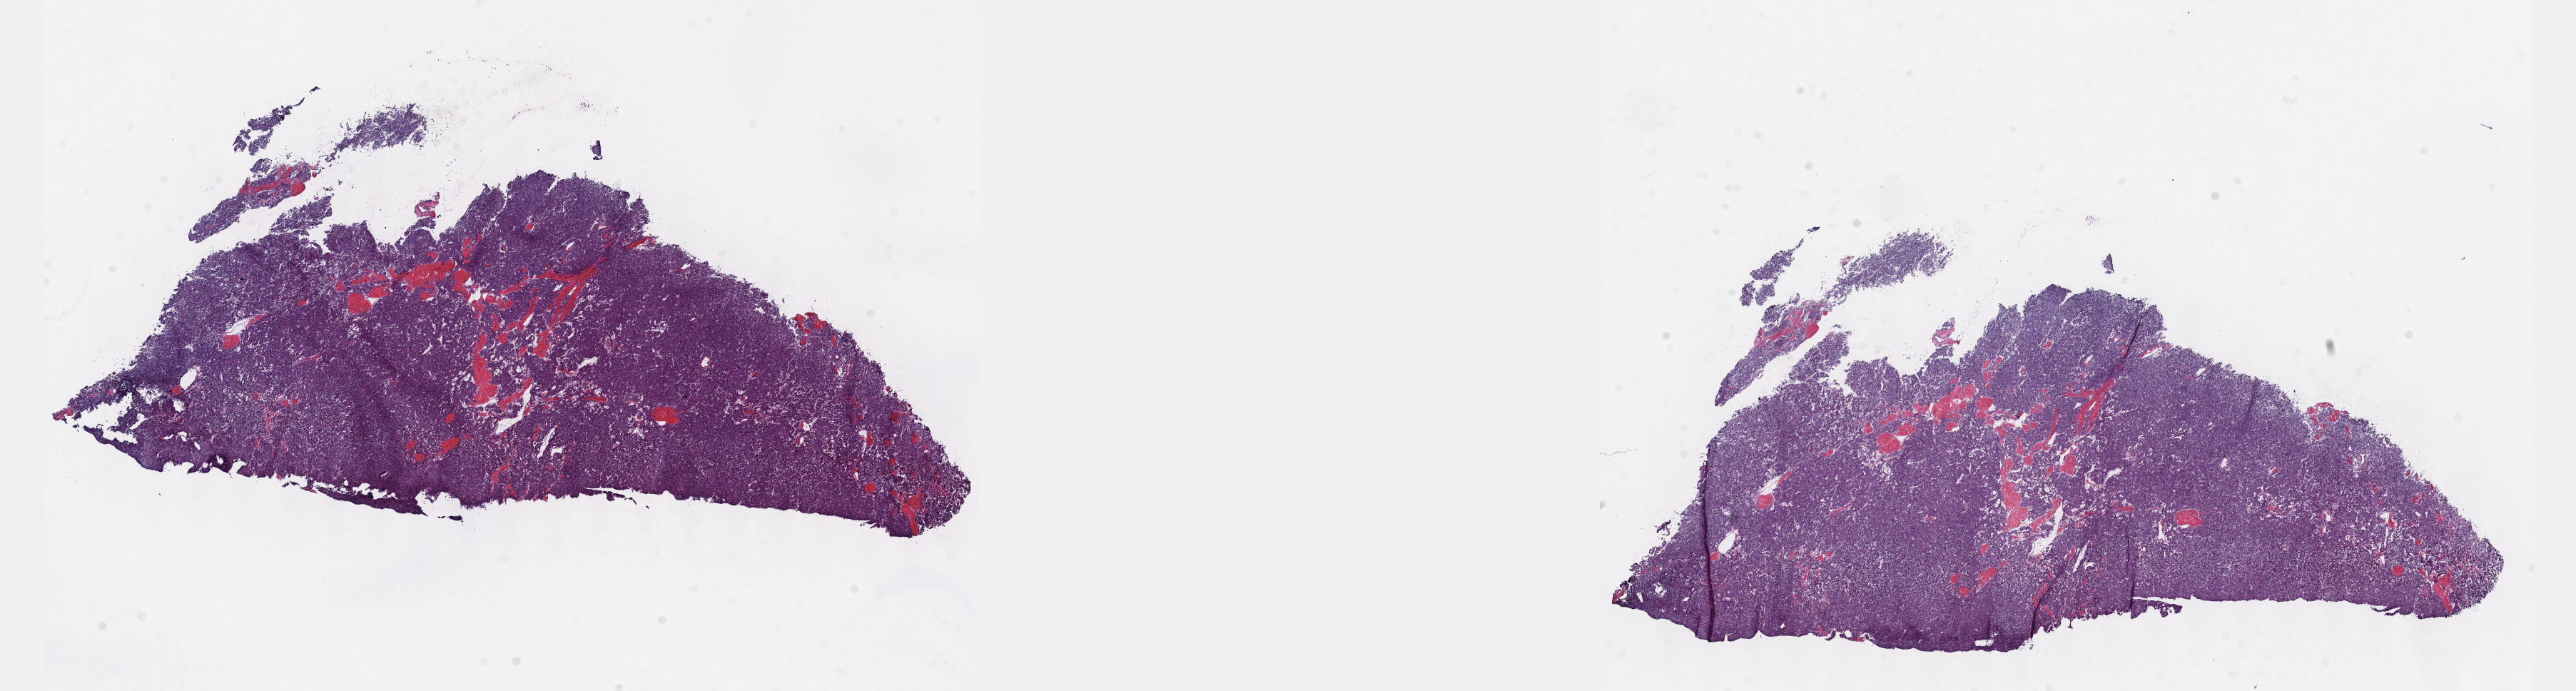
H&E whole-slide image — a low-resolution overview of the entire scanned area, about 29.2 x 7.8 mm; frozen section; thymus, primary tumour sample. Male patient; age at initial diagnosis 73 years. Composition of this section per pathologist review: tumour cells 95%, tumour nuclei 95%, normal cells 0%, stromal cells 5%, necrosis 0%. Infiltration values recorded for this section: lymphocyte infiltration 0%, monocyte infiltration 0%, neutrophil infiltration 0%.
Diagnosis: Thymoma, type A, malignant.